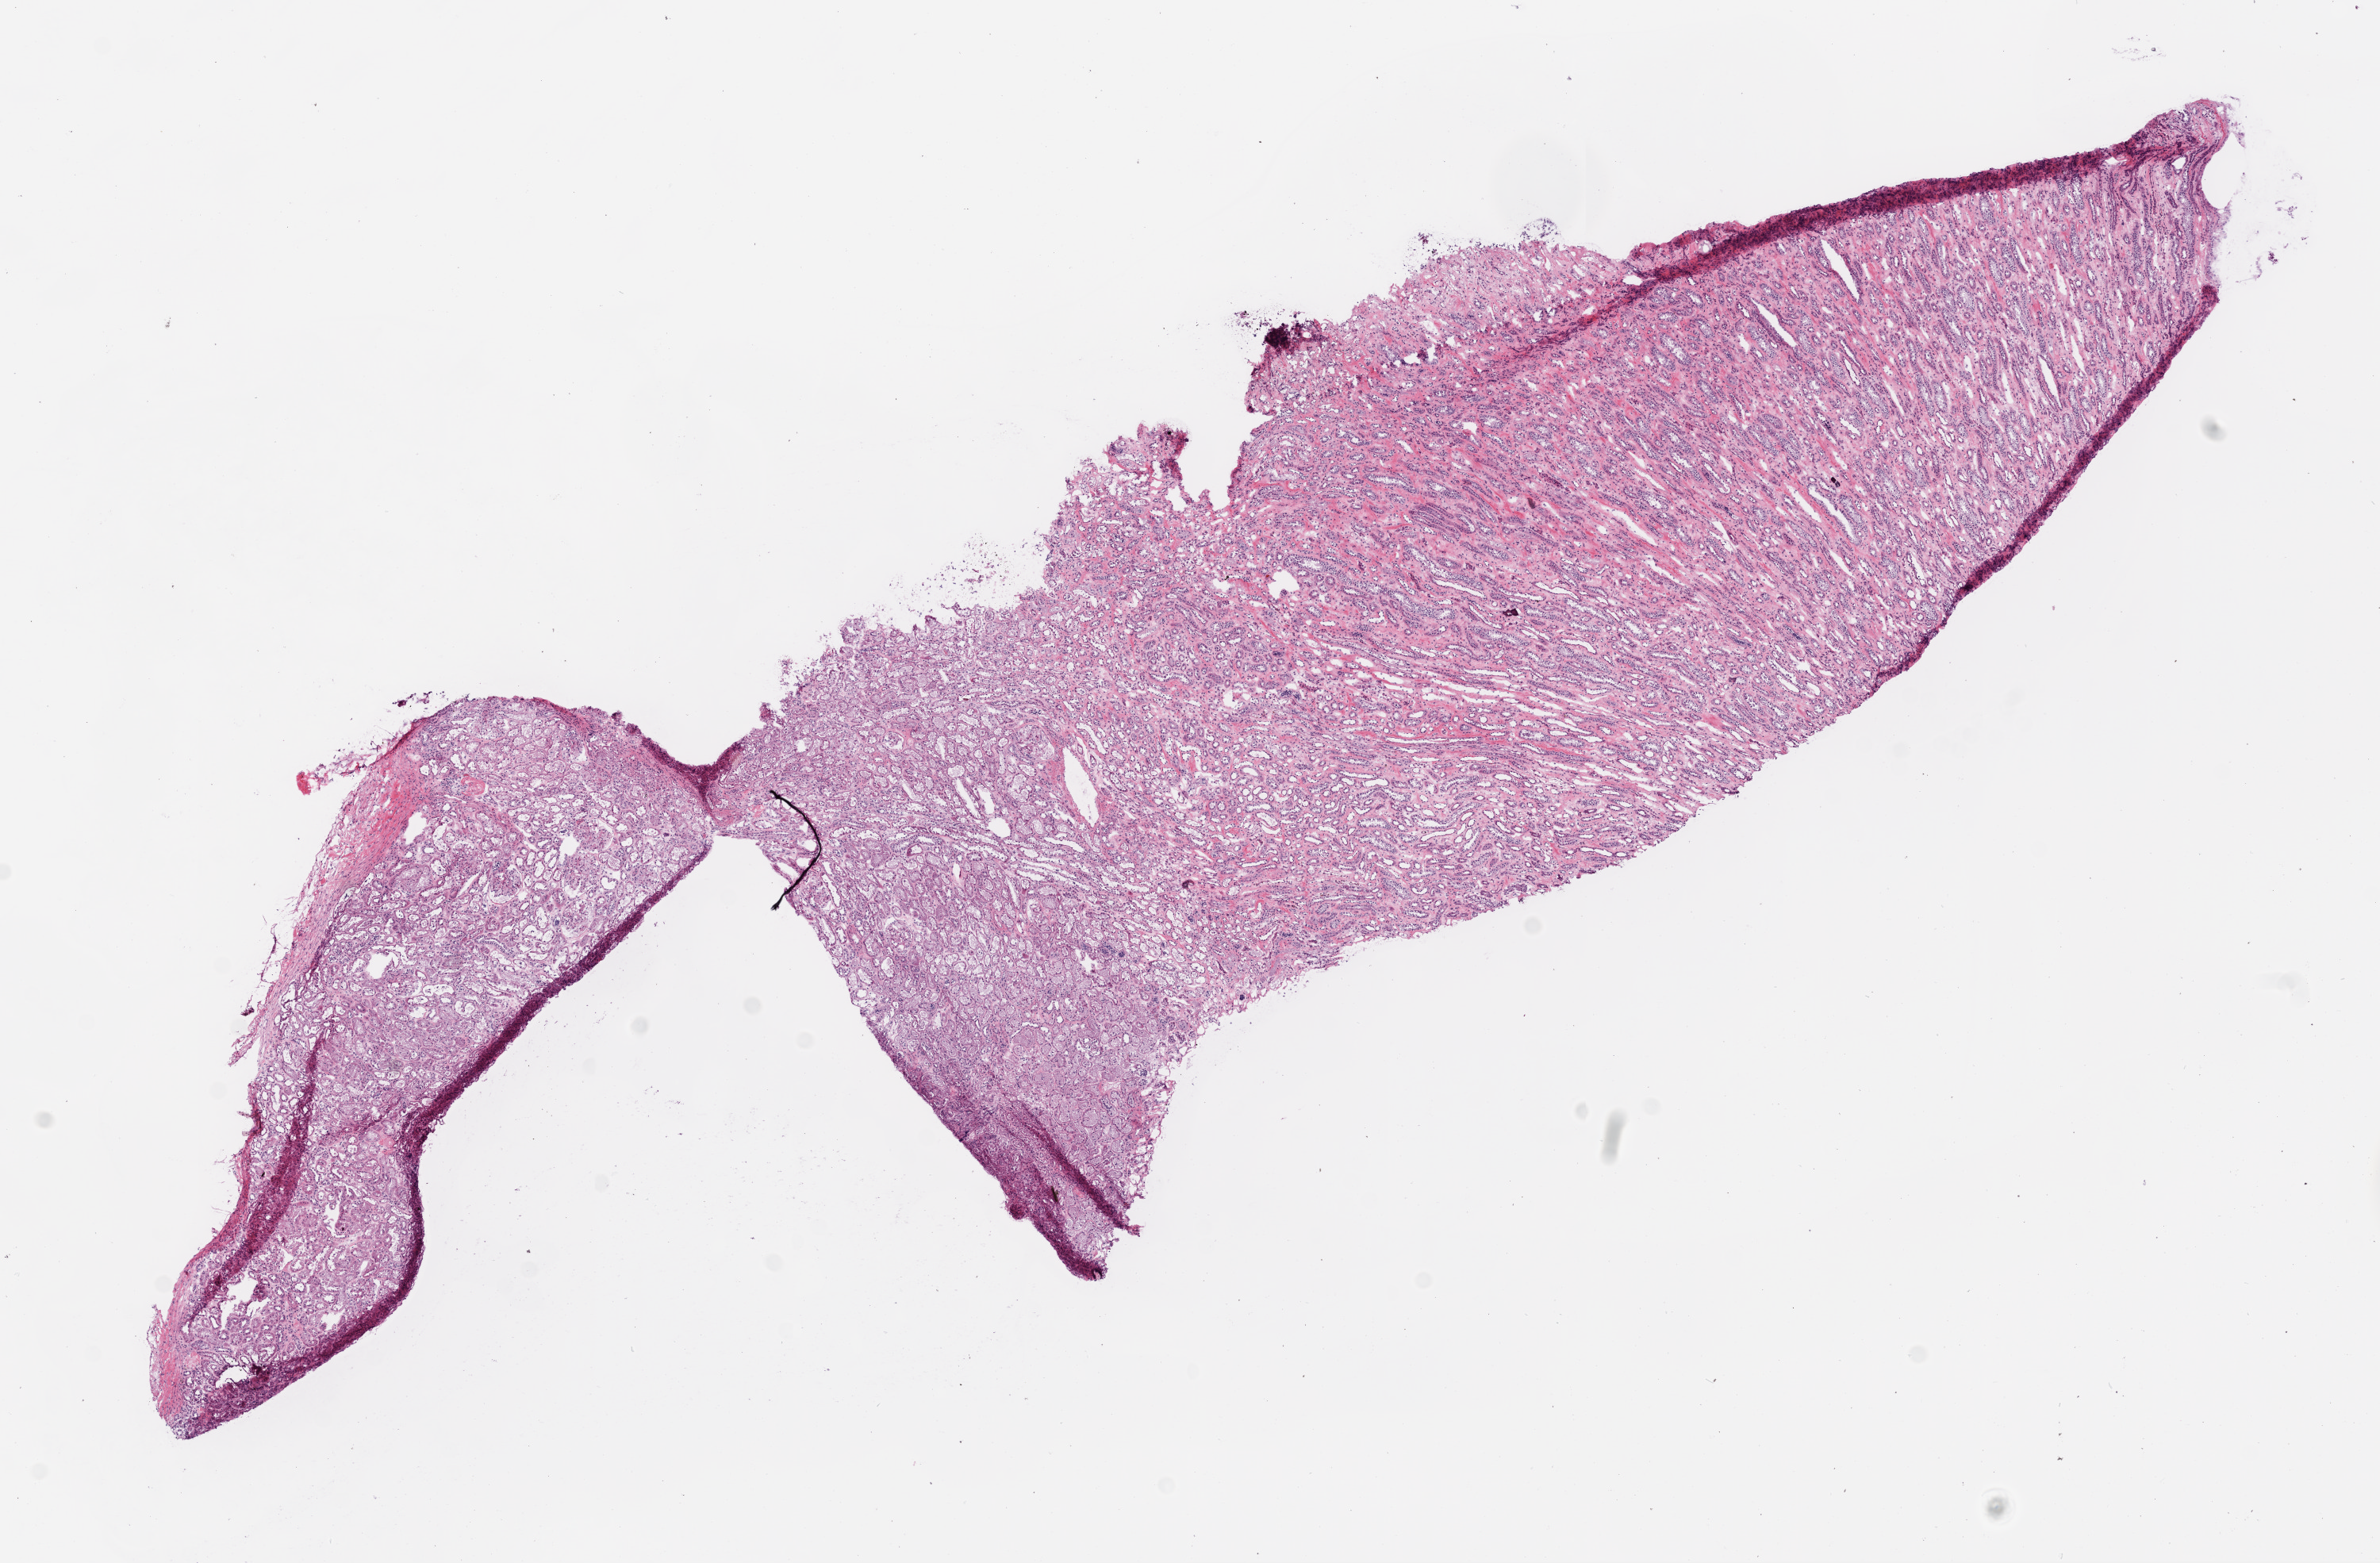
Hematoxylin and eosin (H&E) stained whole-slide image — whole scanned area (about 12.0 x 7.9 mm) shown as a low-resolution overview; frozen section from the top of the tissue portion; sample: solid tissue normal (non-tumour tissue), kidney. Patient: male, age at initial diagnosis 57 years.
This section: solid tissue normal (non-tumour) sample from the same patient. Patient diagnosis: Clear cell adenocarcinoma, NOS.